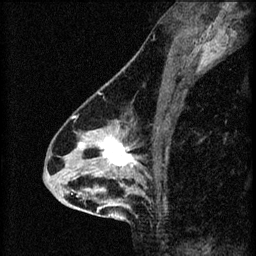
Breast MRI (dynamic contrast-enhanced), one sagittal slice; slice 39 of 60 in the series (ordered by position); 3 images stored at this slice position (order not interpretable as contrast timing); 1.5 T; TE 4.2 ms, TR 8.2 ms; 256 × 256 image matrix, field of view 180 × 180 mm. Female patient, age 46 years.
Annotated regions visible in this slice (semi-automatic segmentation, software-assisted and operator-edited):
- analysis volume of interest (the breast-tissue region the enhancement analysis was run in; not a lesion): bounding box (x1, y1, x2, y2) in pixels: (55, 114, 148, 209)
- tumour enhancement mask (voxels above the 70 % enhancement threshold inside the analysis volume of interest): (71, 116, 139, 169)